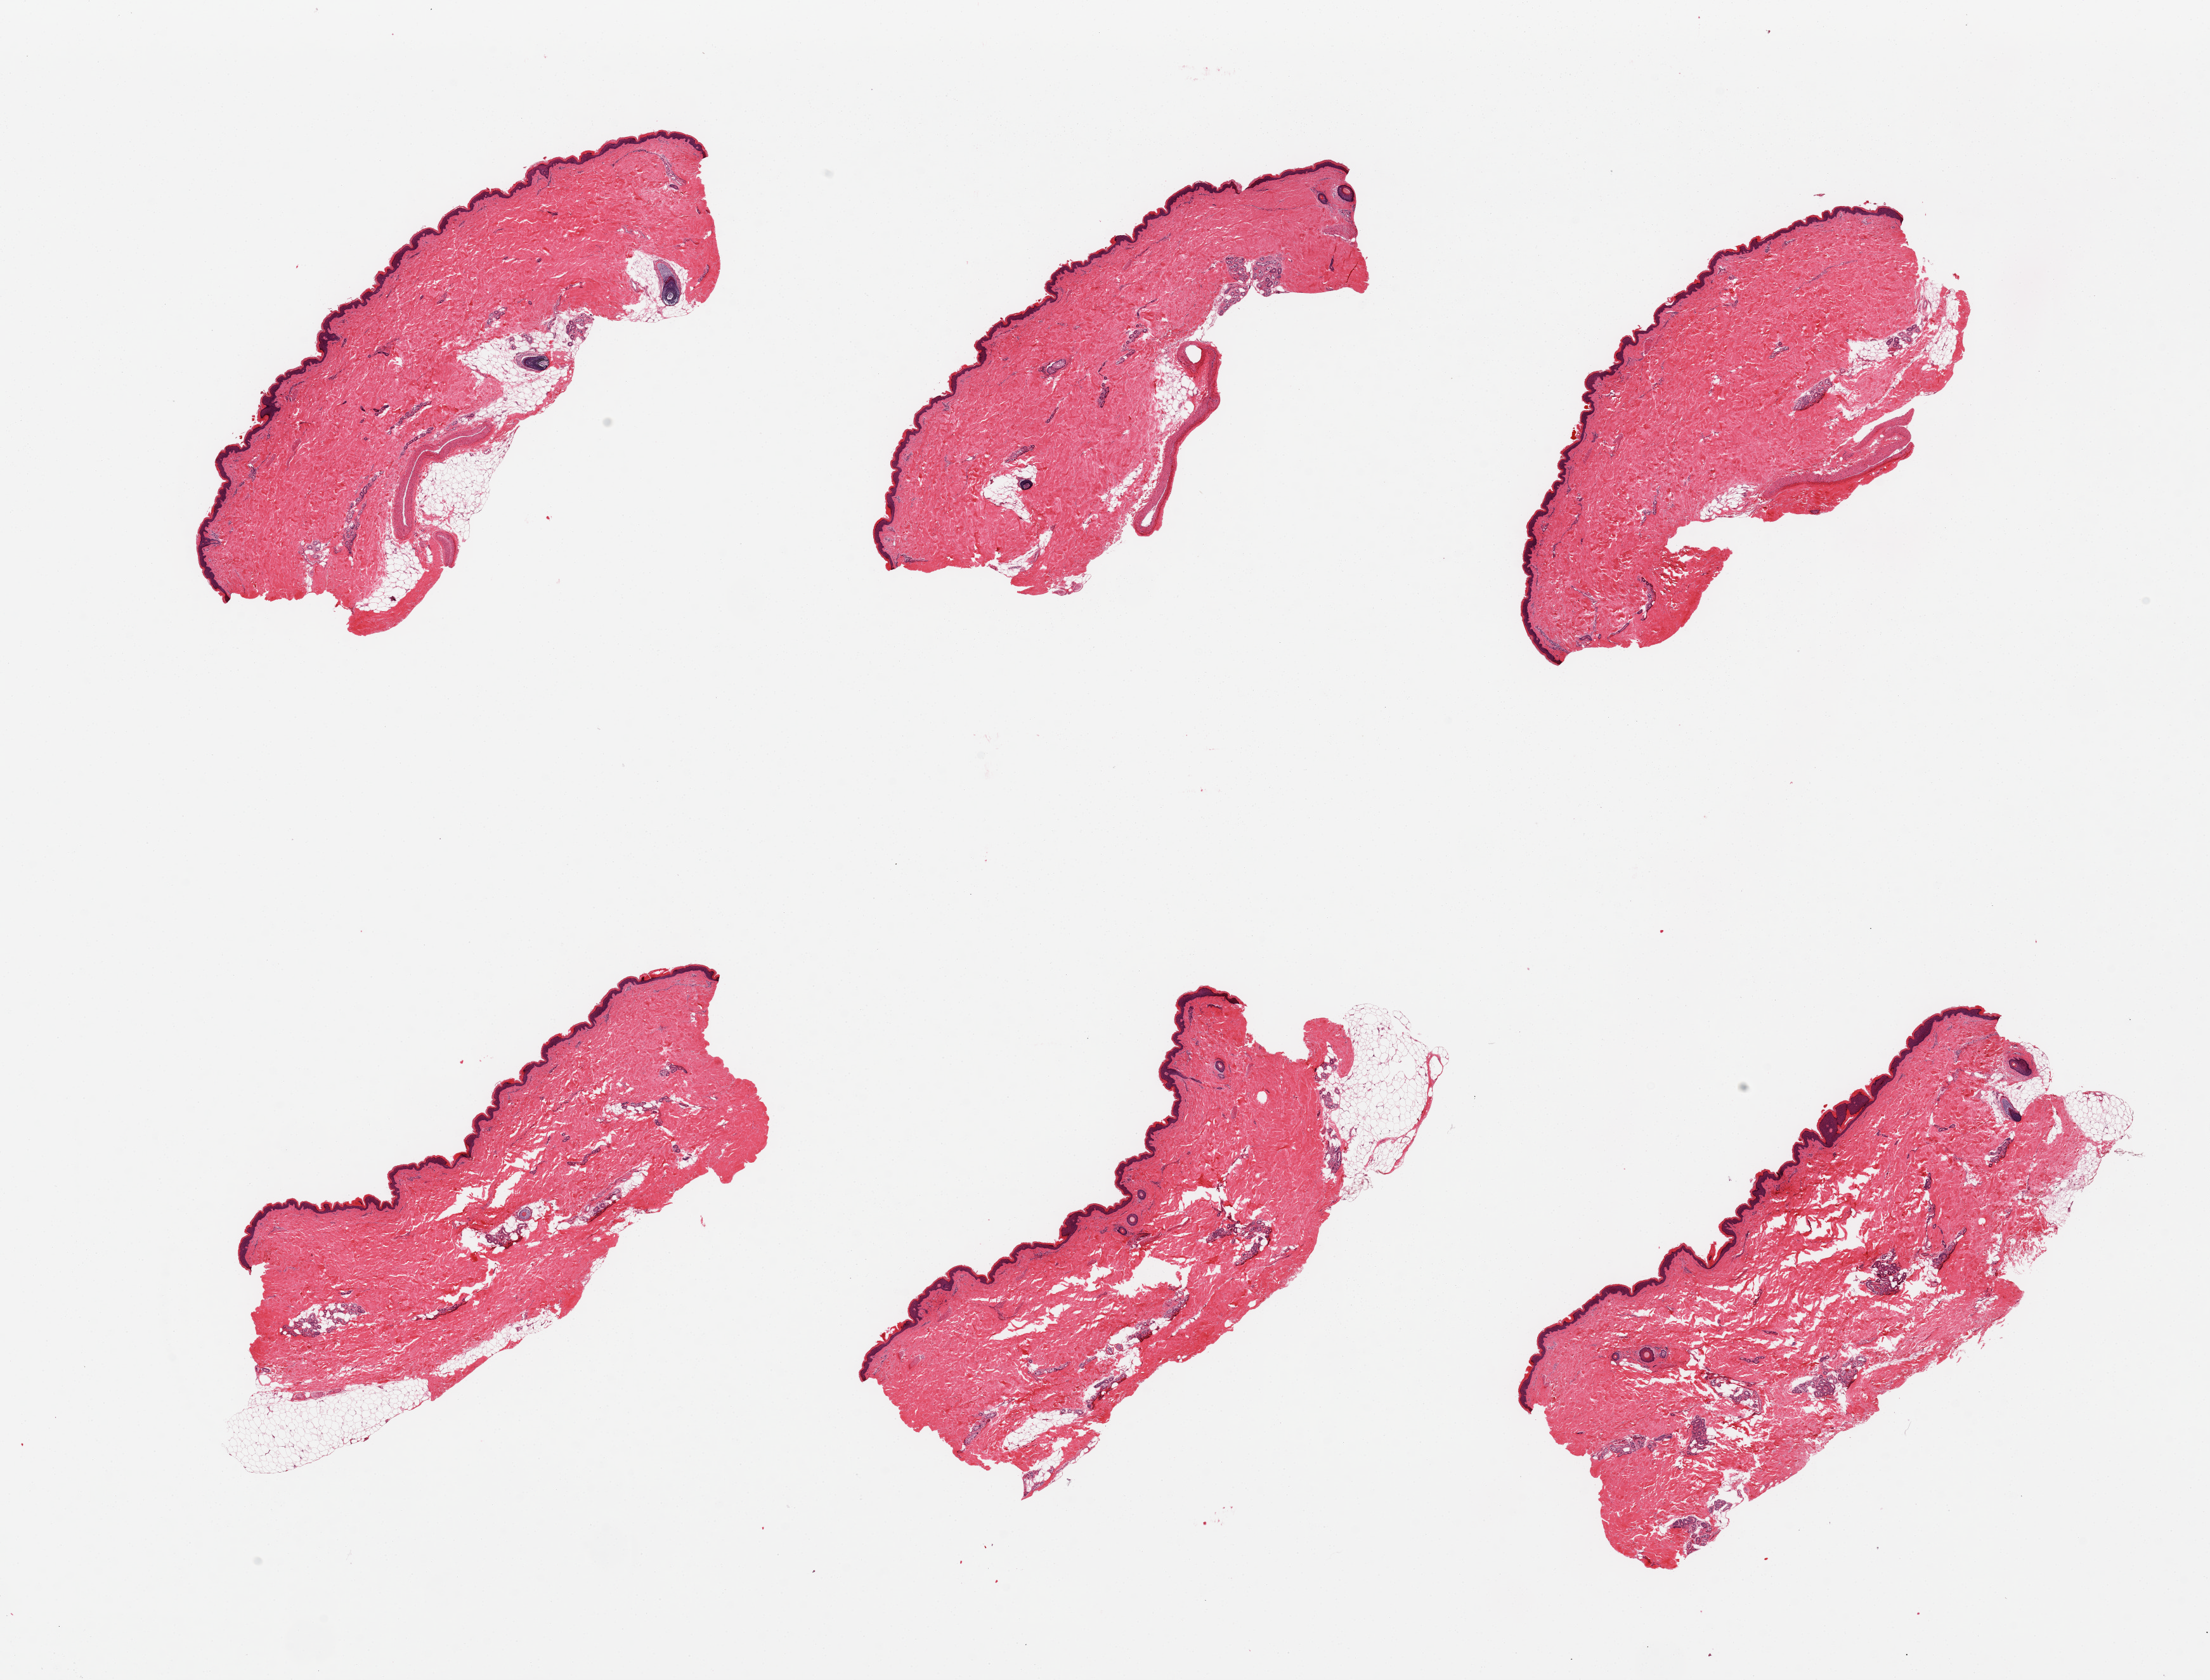
Whole-slide image, hematoxylin and eosin (H&E) stain, shown as a low-resolution overview of the whole scanned area (about 27.6 x 21.0 mm, from a 20x scan). PAXgene-fixed paraffin-embedded (PFPE) section. Sampled site (target tissue): skin of lower leg. Tissue donor sample. Donor: male.
Pathologist's review note for this sample: 6 pieces; small amount of subcutaneous fat and 10% intradermal fat.